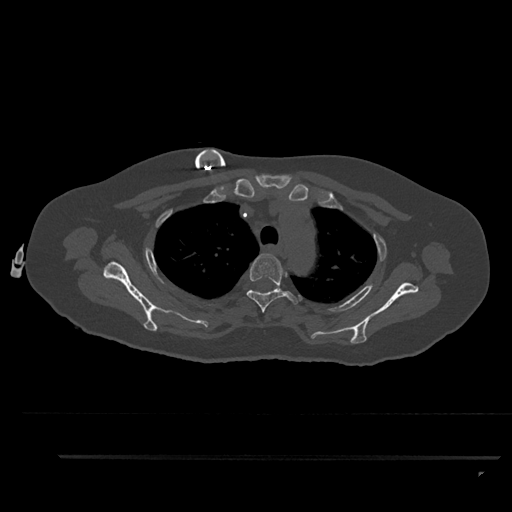
CT including the spine, one axial slice. Slice 682 of 797 in the series (ordered by position). Bone window (W 1800 / L 400 HU). 512 × 512 image matrix. Patient: female, 44 years. Case-level facts recorded for this patient, not image findings: primary cancer: renal; vertebrae with lytic lesions (as recorded): L1.
Structures marked on this image (semi-automatic segmentation, software-assisted and operator-edited):
- T3 vertebra: bounding box (x1, y1, x2, y2) in pixels: (246, 253, 298, 313)